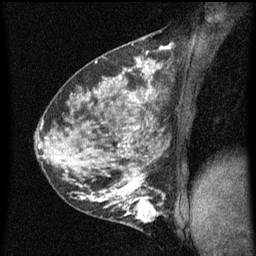
Breast MRI (dynamic contrast-enhanced), one sagittal slice. Position 32 of 60 along the scan axis. Dynamic contrast-enhanced series, image 2 of 5 at this slice position (ordered by acquisition). 1.5 T. TE 4.2 ms, TR 8 ms. 2 mm slice thickness. 256 × 256 image matrix, field of view 180 × 180 mm. Female patient, age 35 years.
Structures marked on this image (semi-automatically segmented with operator editing):
- analysis volume of interest (the breast-tissue region the enhancement analysis was run in; not a lesion): box from (x=118, y=190) to (x=165, y=229) px
- tumour enhancement mask (voxels above the 70 % enhancement threshold inside the analysis volume of interest): (x=118, y=190)–(x=165, y=223)